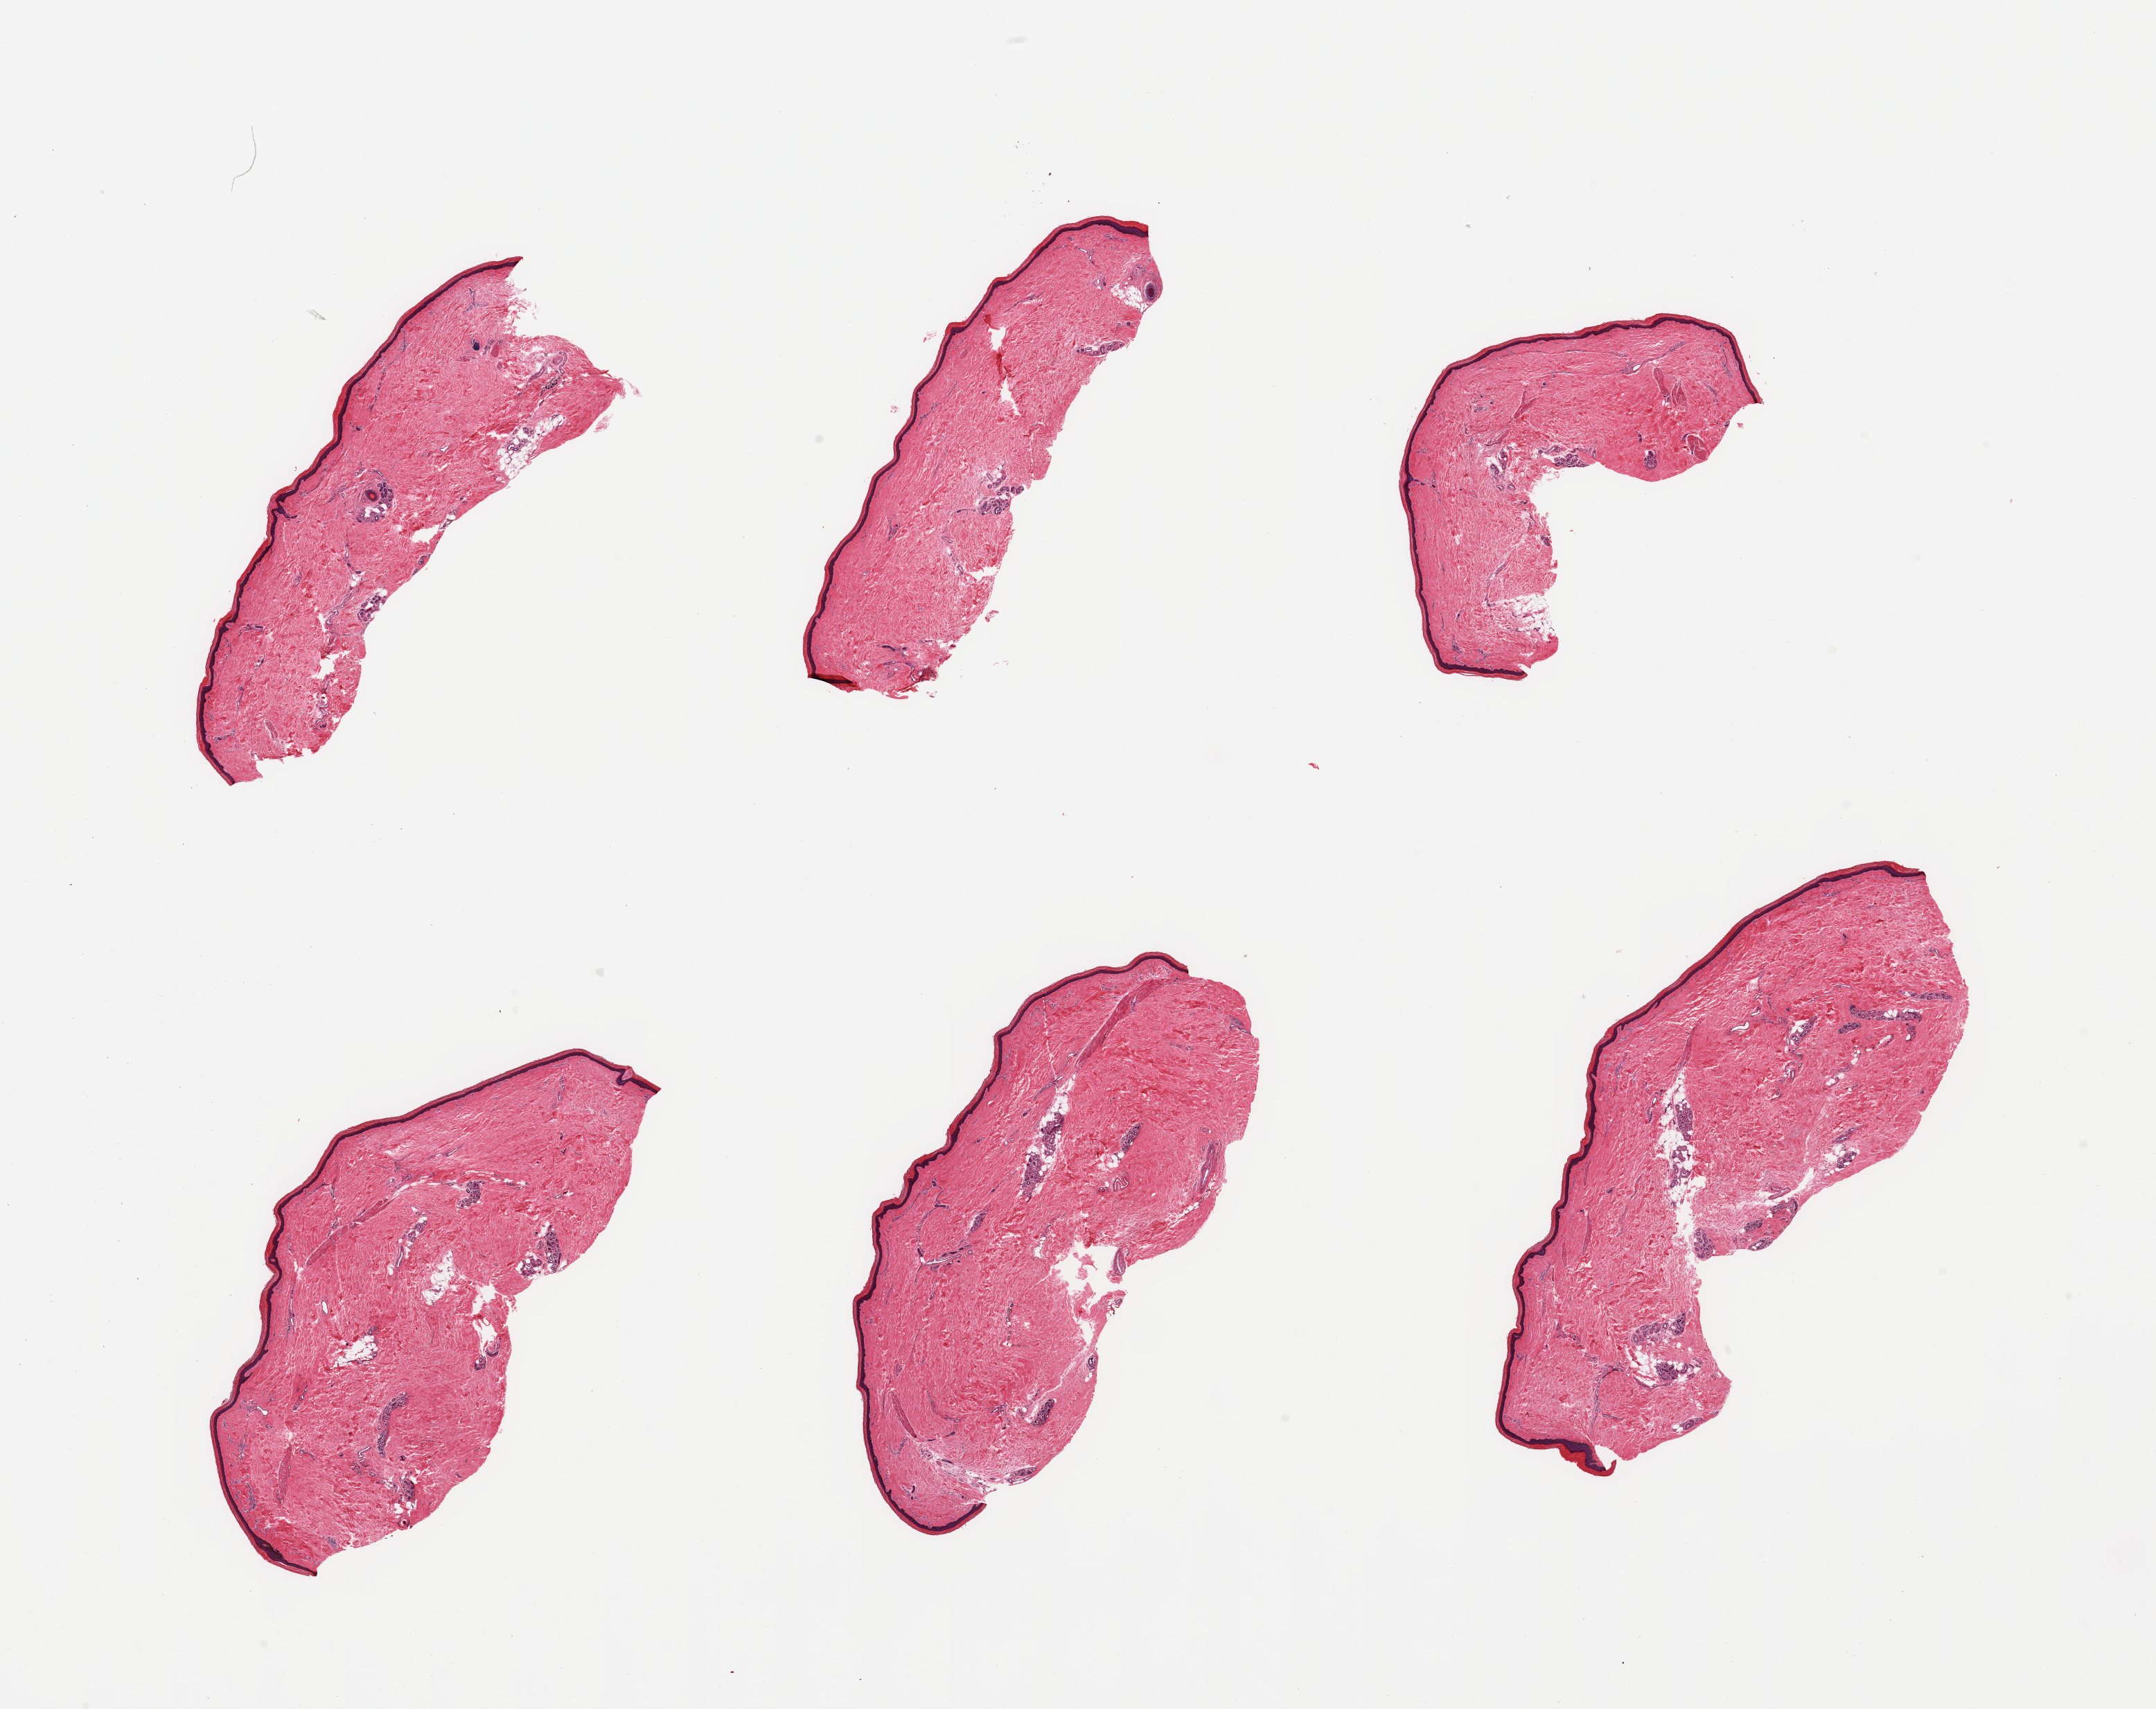
Haematoxylin and eosin whole-slide image, shown as a low-resolution overview of the whole scanned area (about 24.6 x 19.5 mm, from a 20x scan); PAXgene-fixed, paraffin-embedded tissue; target tissue: skin of lower leg; tissue donor sample. Donor: male.
Review note (as recorded): 6 pieces; well trimmed skin; periadnexal fat; ~37.4 microns epidermis.